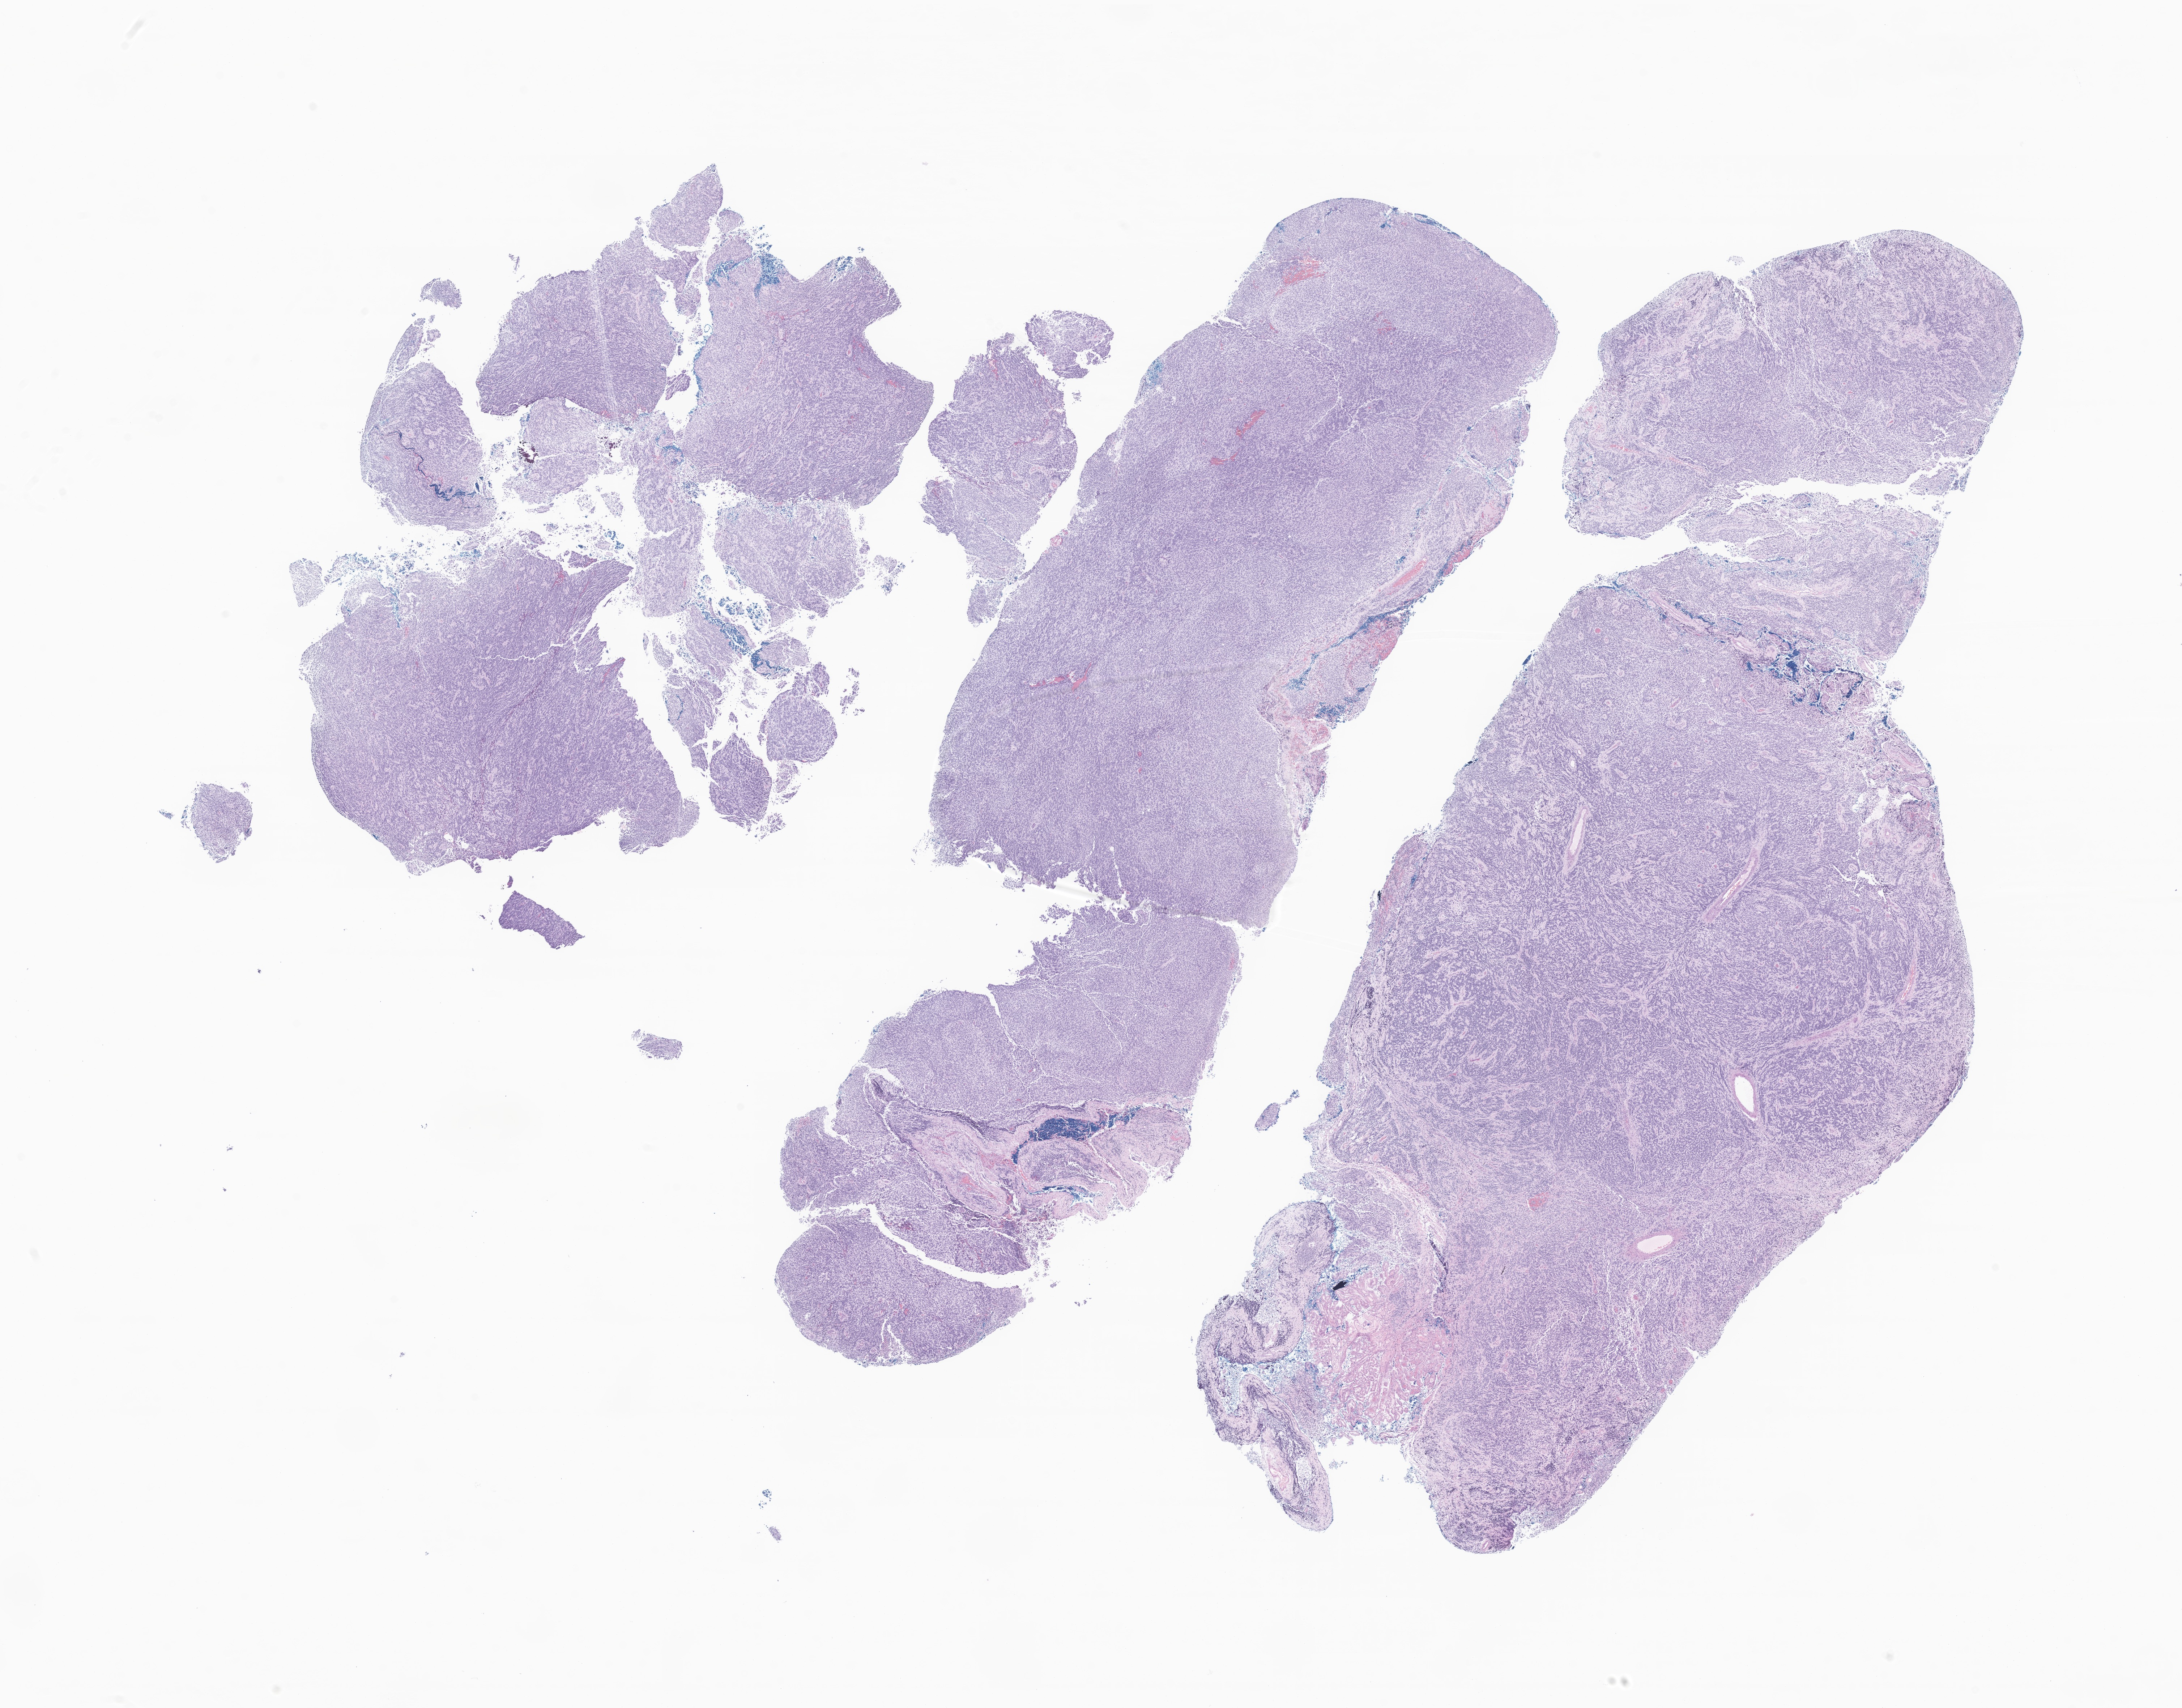
Hematoxylin and eosin (H&E) whole-slide image of tumor tissue from the cerebellum, a low-resolution overview of the entire scanned area, about 25.4 x 19.9 mm. Formalin-fixed, paraffin-embedded (FFPE) tissue. Patient male; age 183 months.
Diagnosis (ICD-O-3 morphology term): Medulloblastoma, NOS.